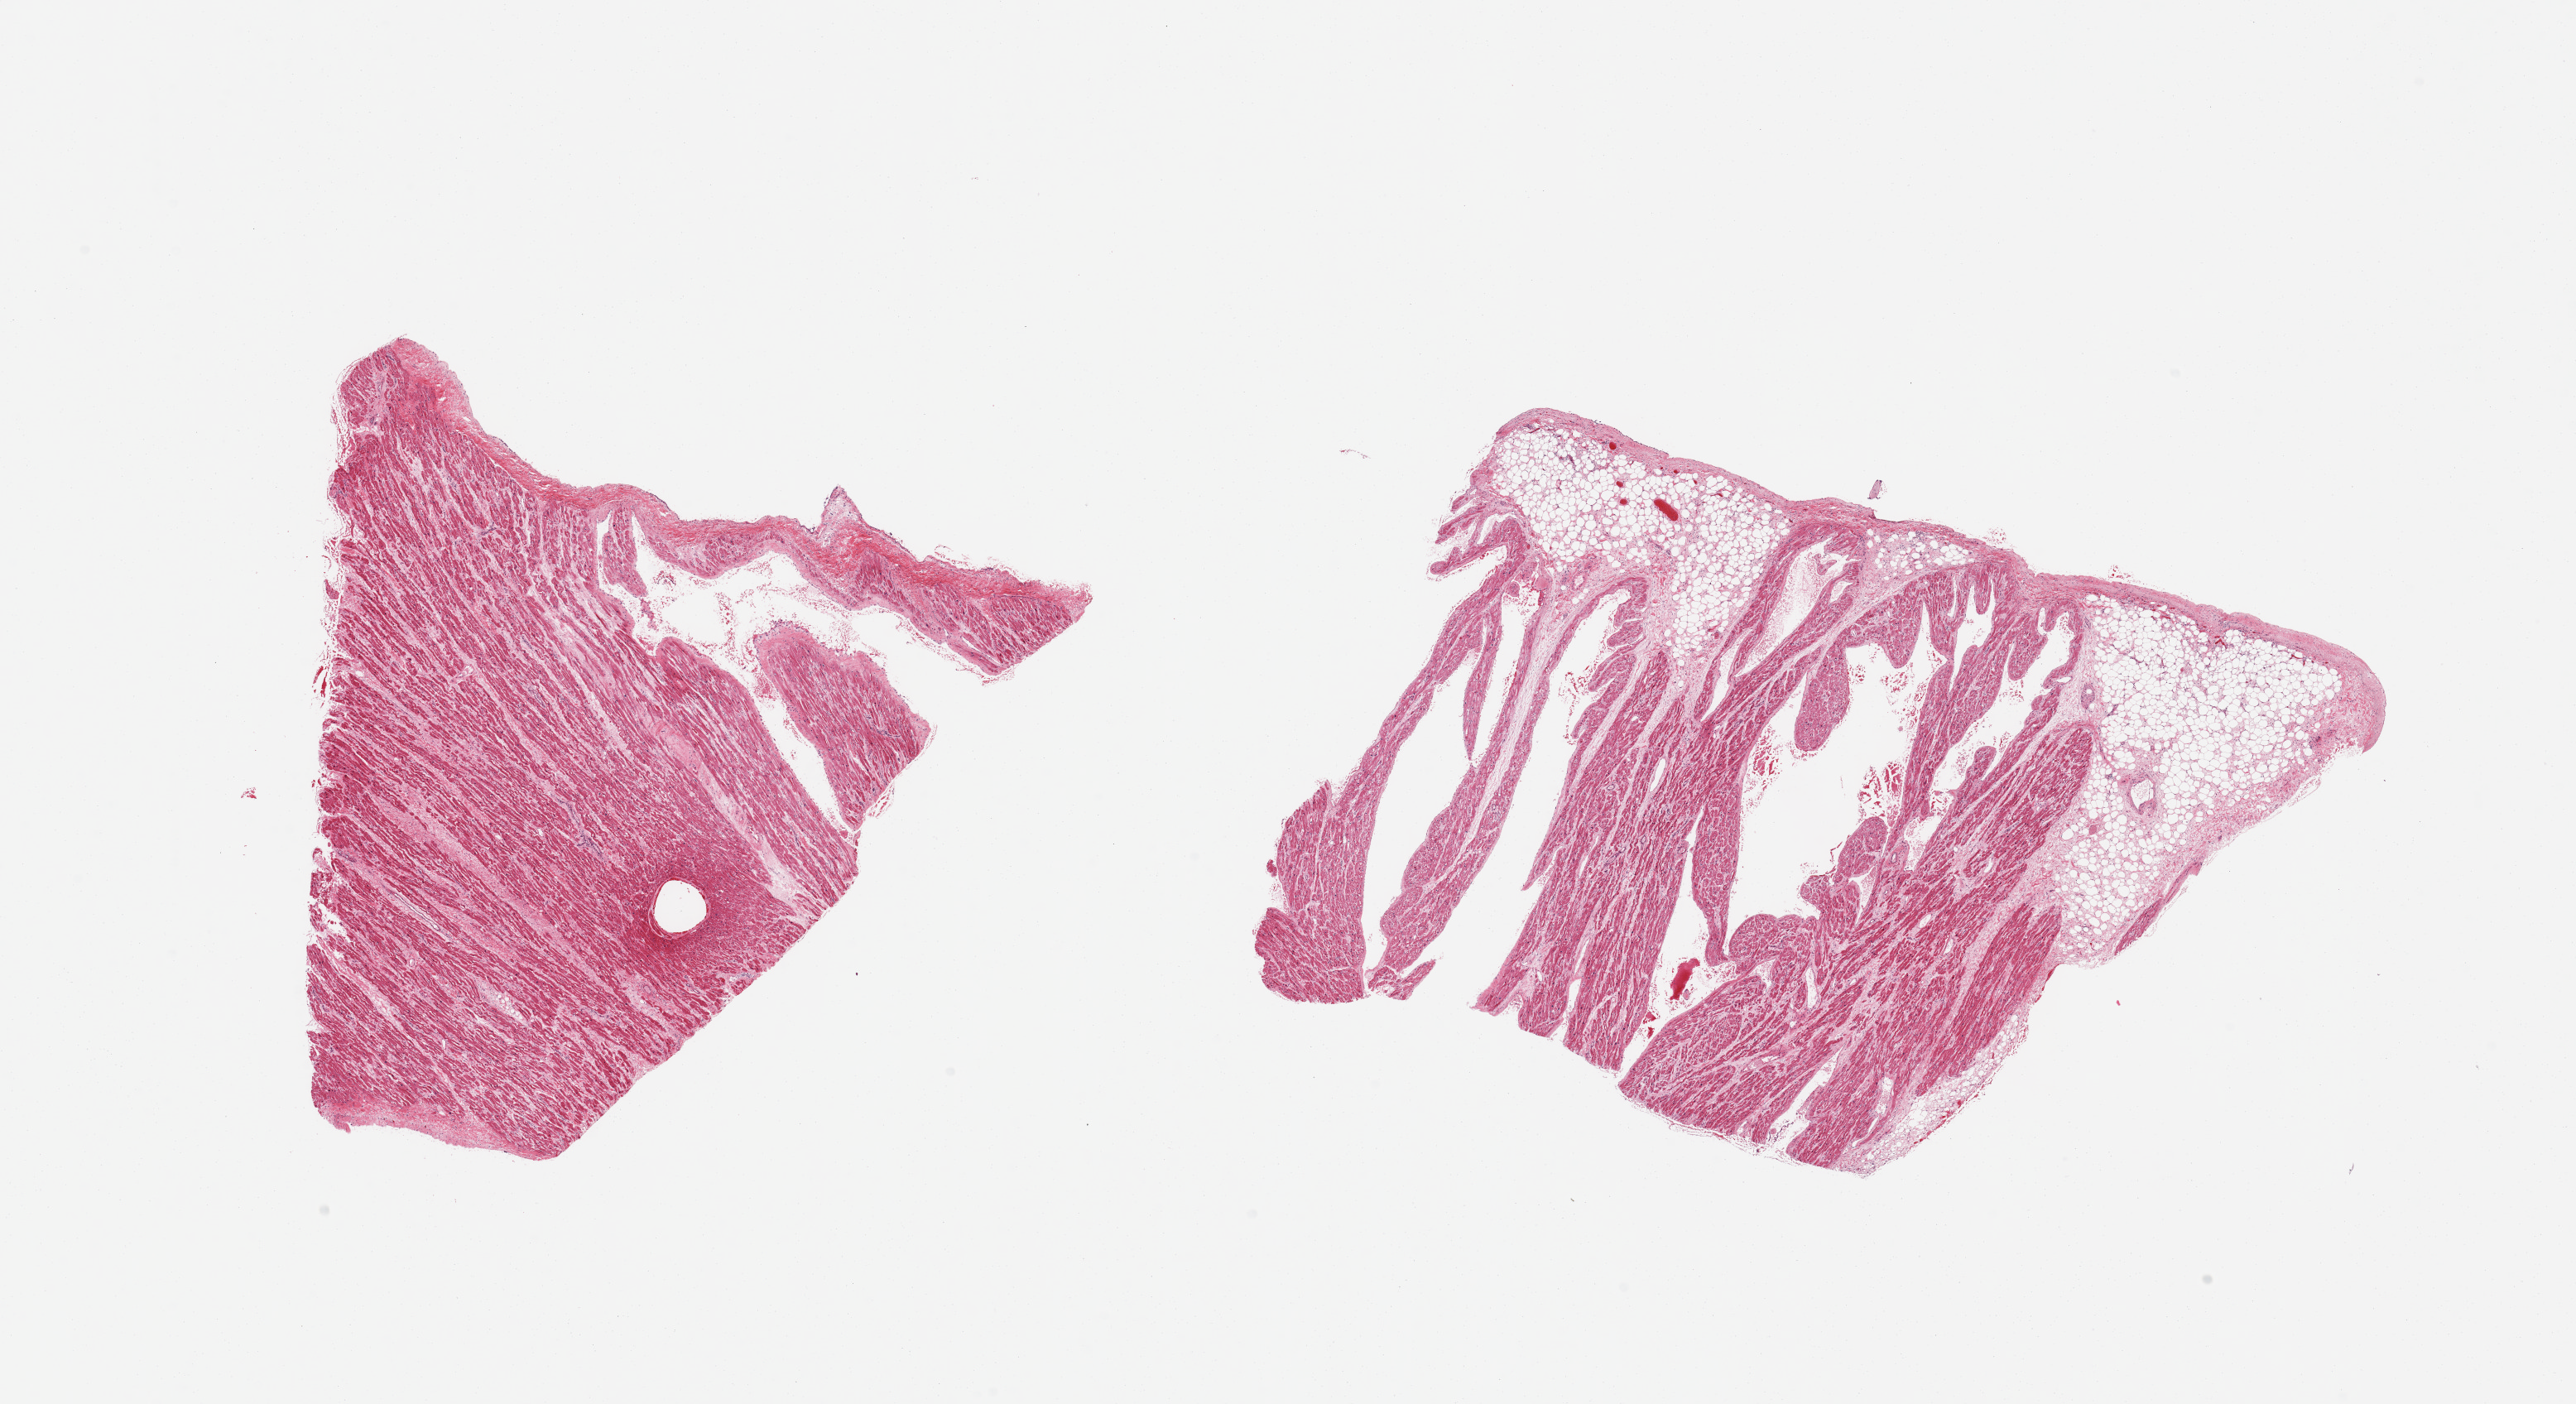
Whole-slide image, H&E stain, whole scanned area (about 24.6 x 13.4 mm, acquisition: 20x scan) shown as a low-resolution overview. PAXgene-fixed, paraffin-embedded tissue. Target tissue: auricular appendage. Donor tissue sample.
Review note (as recorded): 2 pieces; interstitial fibrosis, 25% of 1 piece is fat.